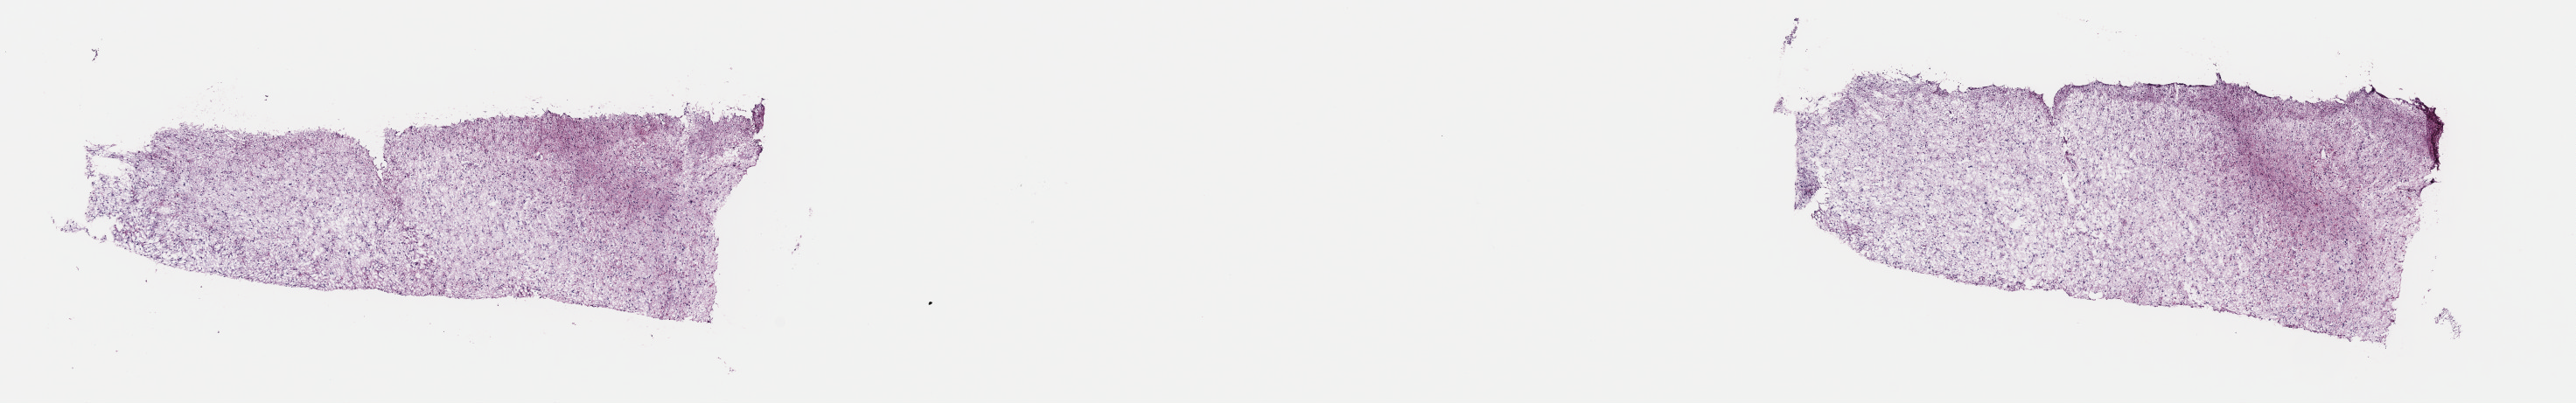
Hematoxylin and eosin (H&E) stained whole-slide image, whole scanned area (about 23.2 x 3.6 mm, from a 40x scan) shown as a low-resolution overview, frozen section from the top of the tissue portion, brain, primary tumour sample. Male, age 36 years at initial diagnosis. Histologic grade: G3 (poorly differentiated). Slide review estimates, as recorded: tumour cells 30%, tumour nuclei 80%, normal cells 10%, stromal cells 60%, necrosis 0%. Infiltration values recorded for this section: lymphocyte infiltration 0%, monocyte infiltration 0%, neutrophil infiltration 0%.
* diagnosis: Astrocytoma, anaplastic (cerebrum)